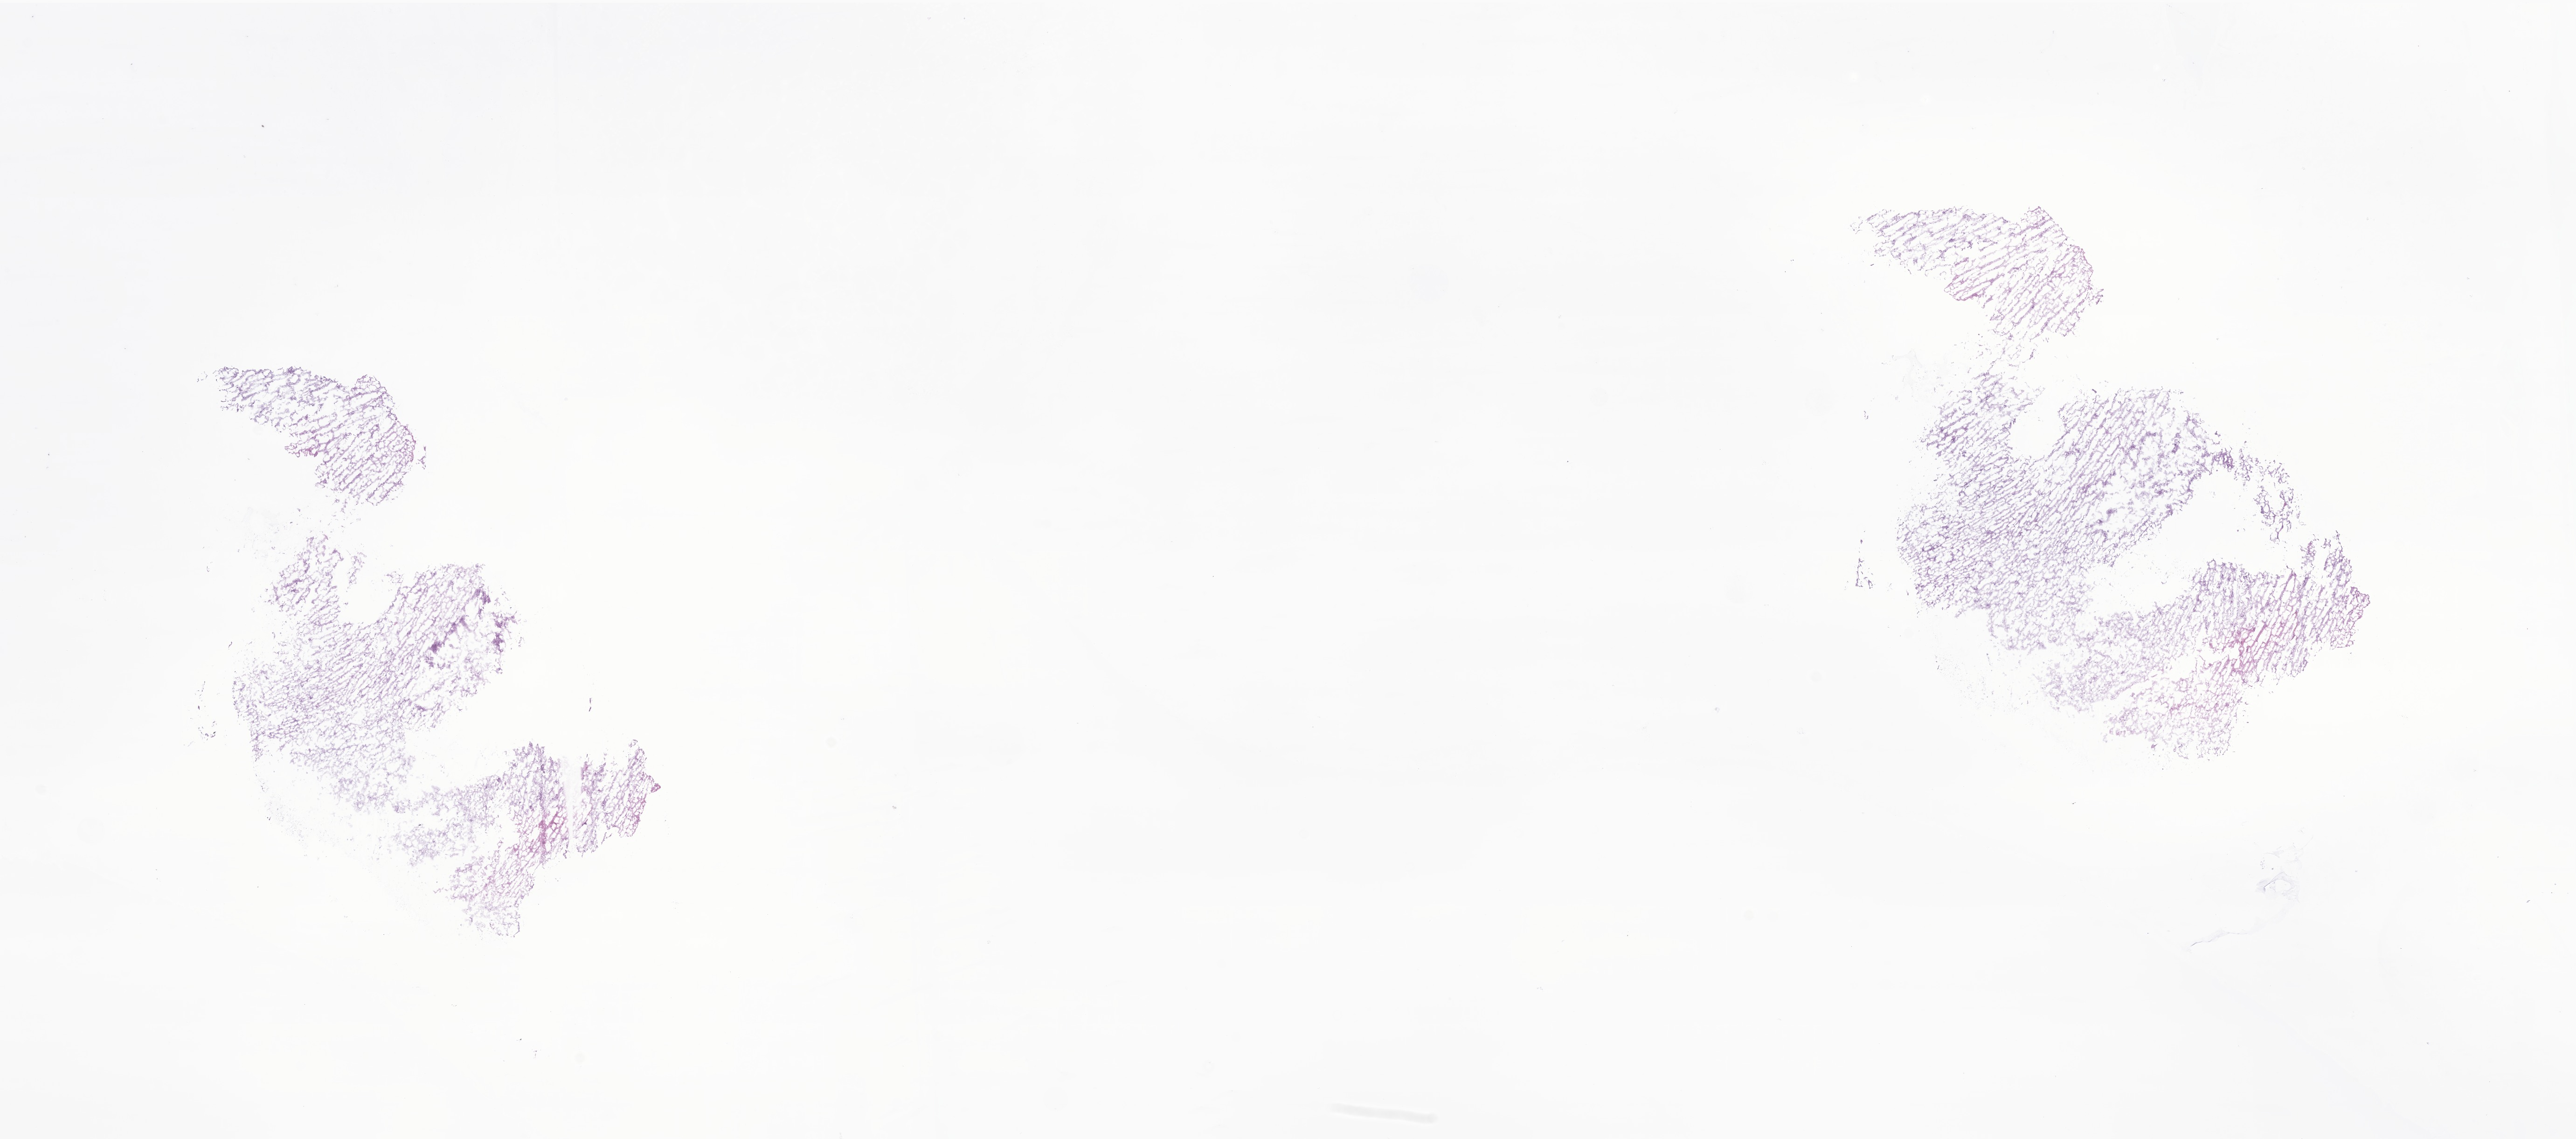
Whole-slide image, haematoxylin and eosin stain of tumor tissue from the brain, low-resolution overview of the scanned area, about 23.3 x 10.3 mm; frozen section (OCT-embedded). Patient female; age 190 months (15 years 10 months).
Recorded diagnosis: Glioma, malignant.